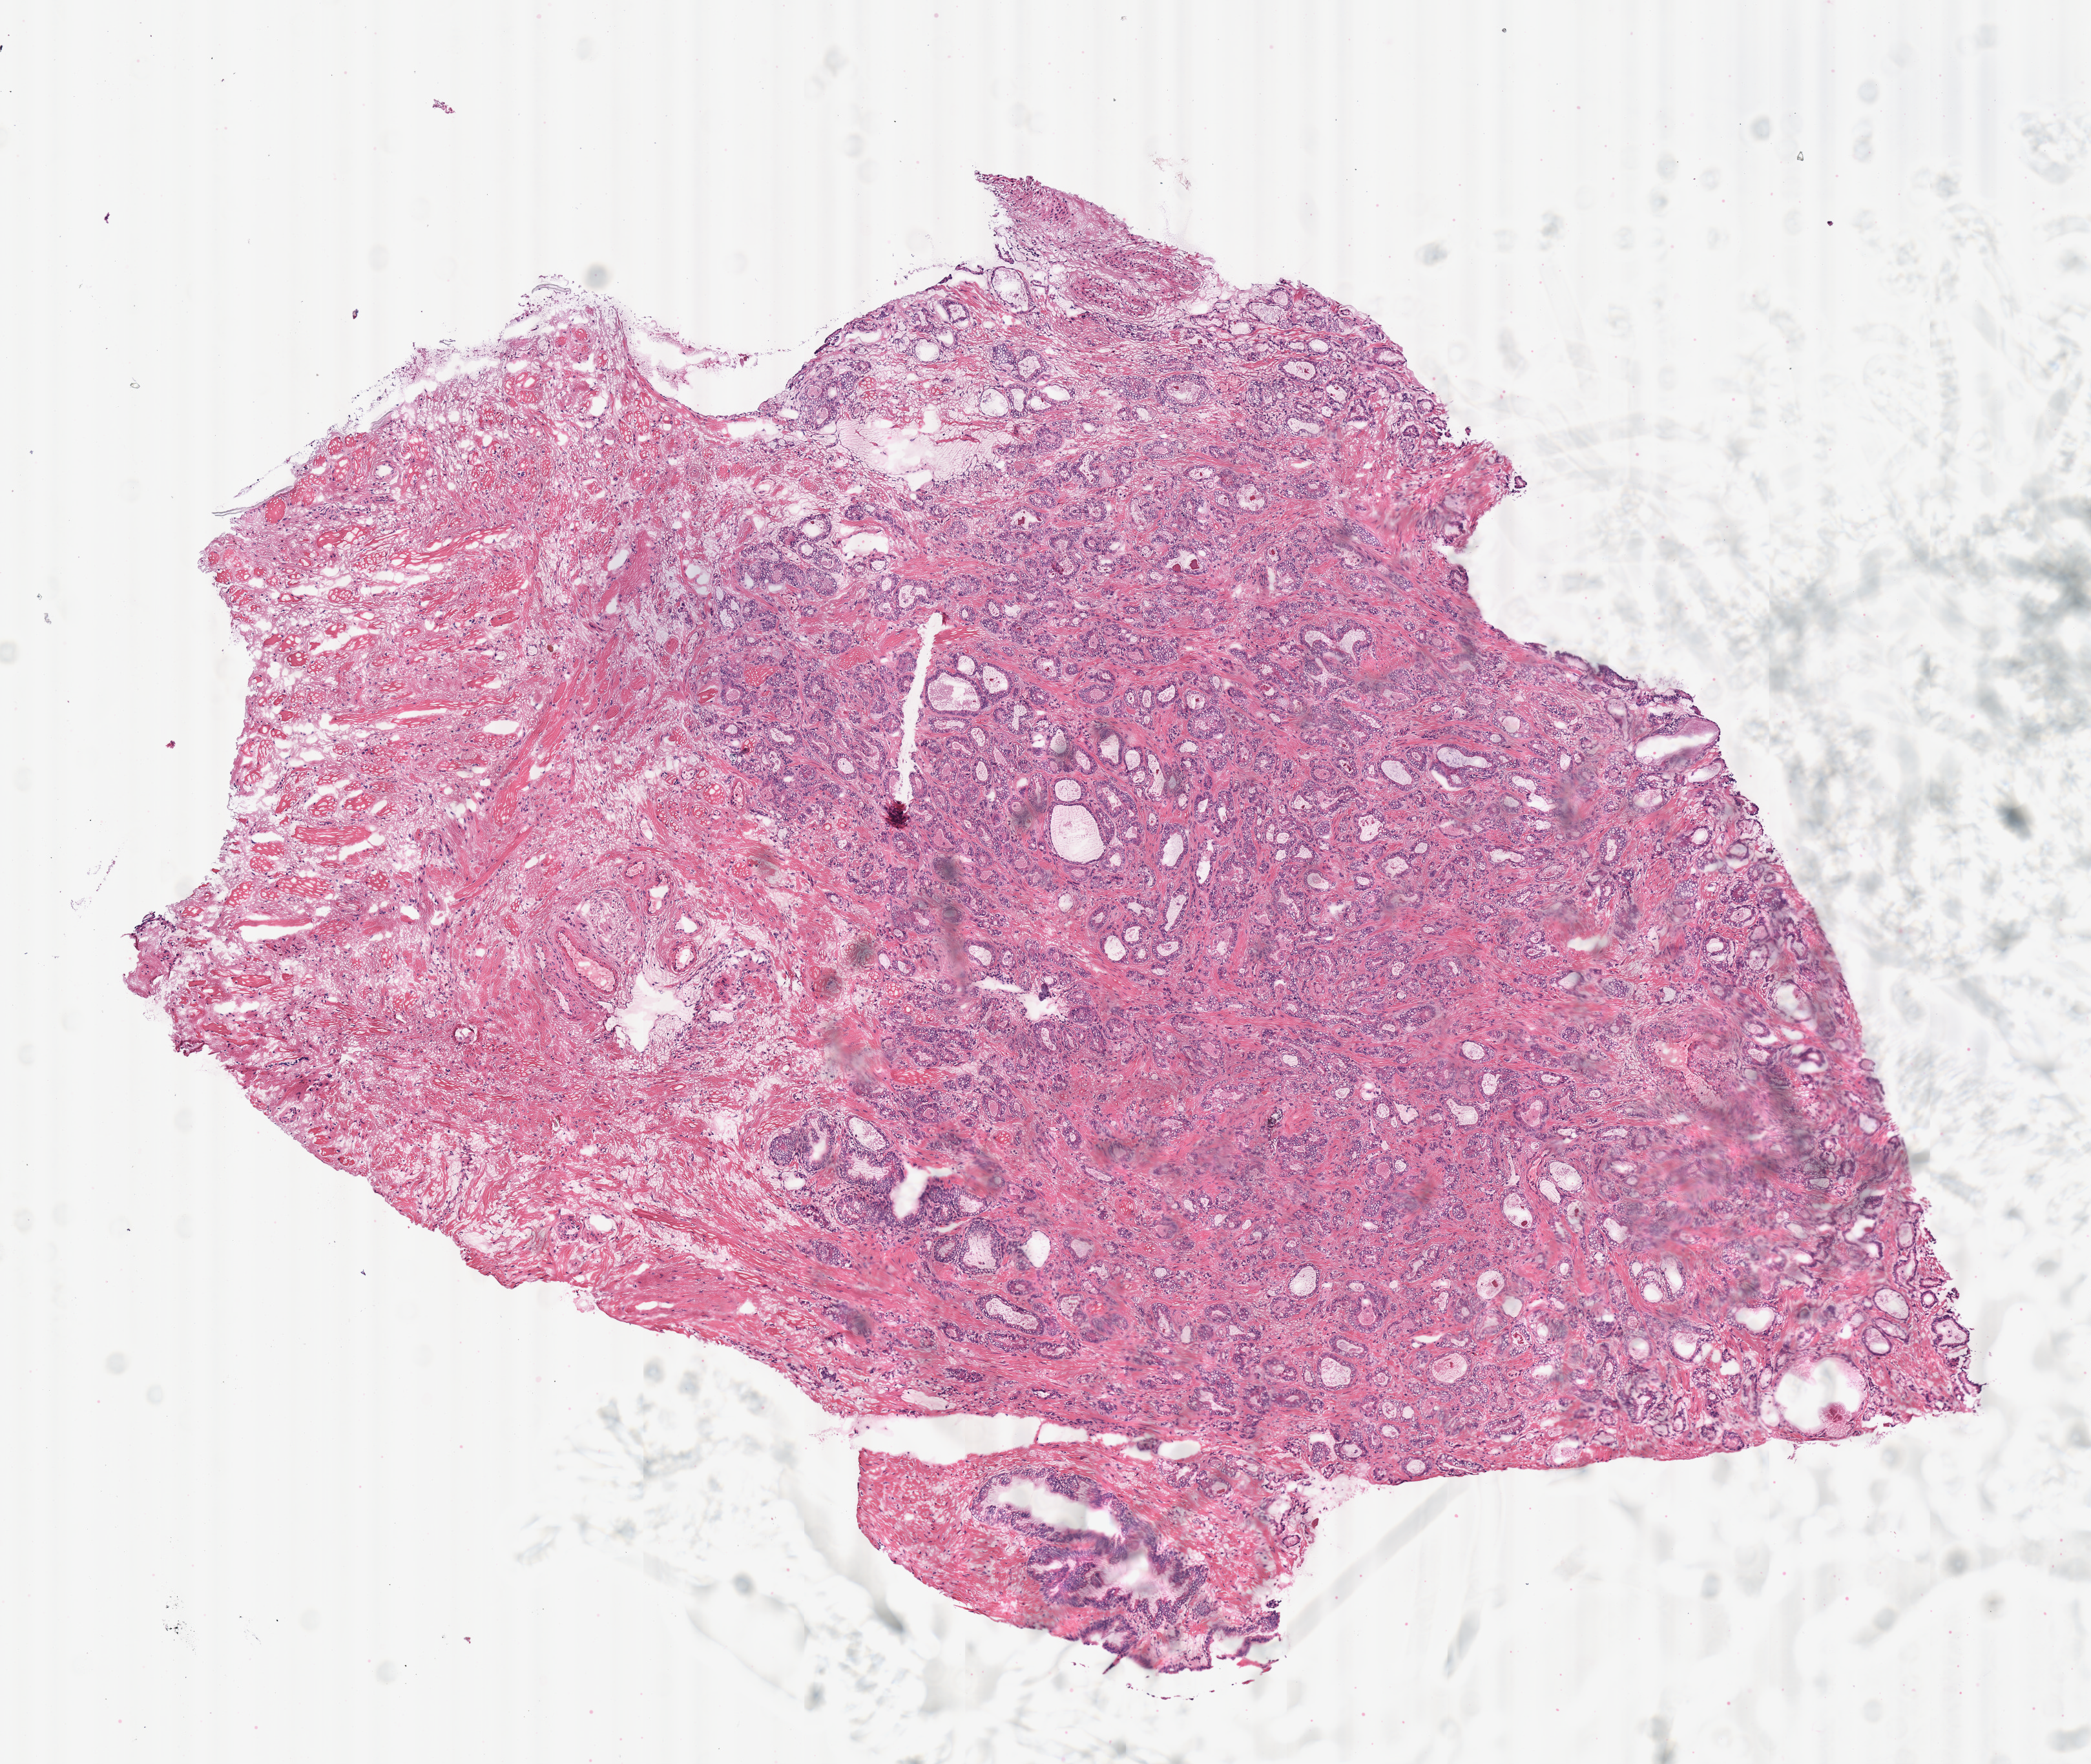
H&E-stained whole-slide image — shown as a low-resolution overview of the whole scanned area (about 6.4 x 5.4 mm), frozen section from the top of the tissue portion, primary tumour sample from the prostate. Male, age 47 years at initial diagnosis. Gleason score: 7 (3+4). Slide review estimates, as recorded: tumour cells 60%, tumour nuclei 60%, normal cells 10%, stromal cells 30%, necrosis 0%.
- lymph nodes positive (case pathology): 0 of 4 examined
- diagnosis: Acinar cell carcinoma (prostate gland)
- laterality: bilateral